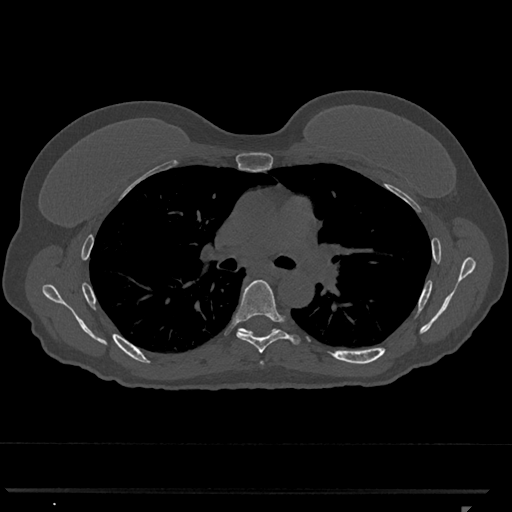
CT including the spine, one axial slice; position 756 of 793 along the scan axis; reconstruction kernel Br40s/3; 120 kVp; bone window (W 1800 / L 400 HU); 0.5 mm slice thickness; 512 × 512 image matrix. Patient: female, 62 years. Case-level facts recorded for this patient, not image findings: primary cancer: renal.
Outlined on this slice (semi-automatically segmented with operator editing):
- T5 vertebra: bounding box [x1, y1, x2, y2] px = [260, 361, 264, 365]
- T6 vertebra: [235, 279, 300, 354]
- T7 vertebra: [241, 328, 253, 333]